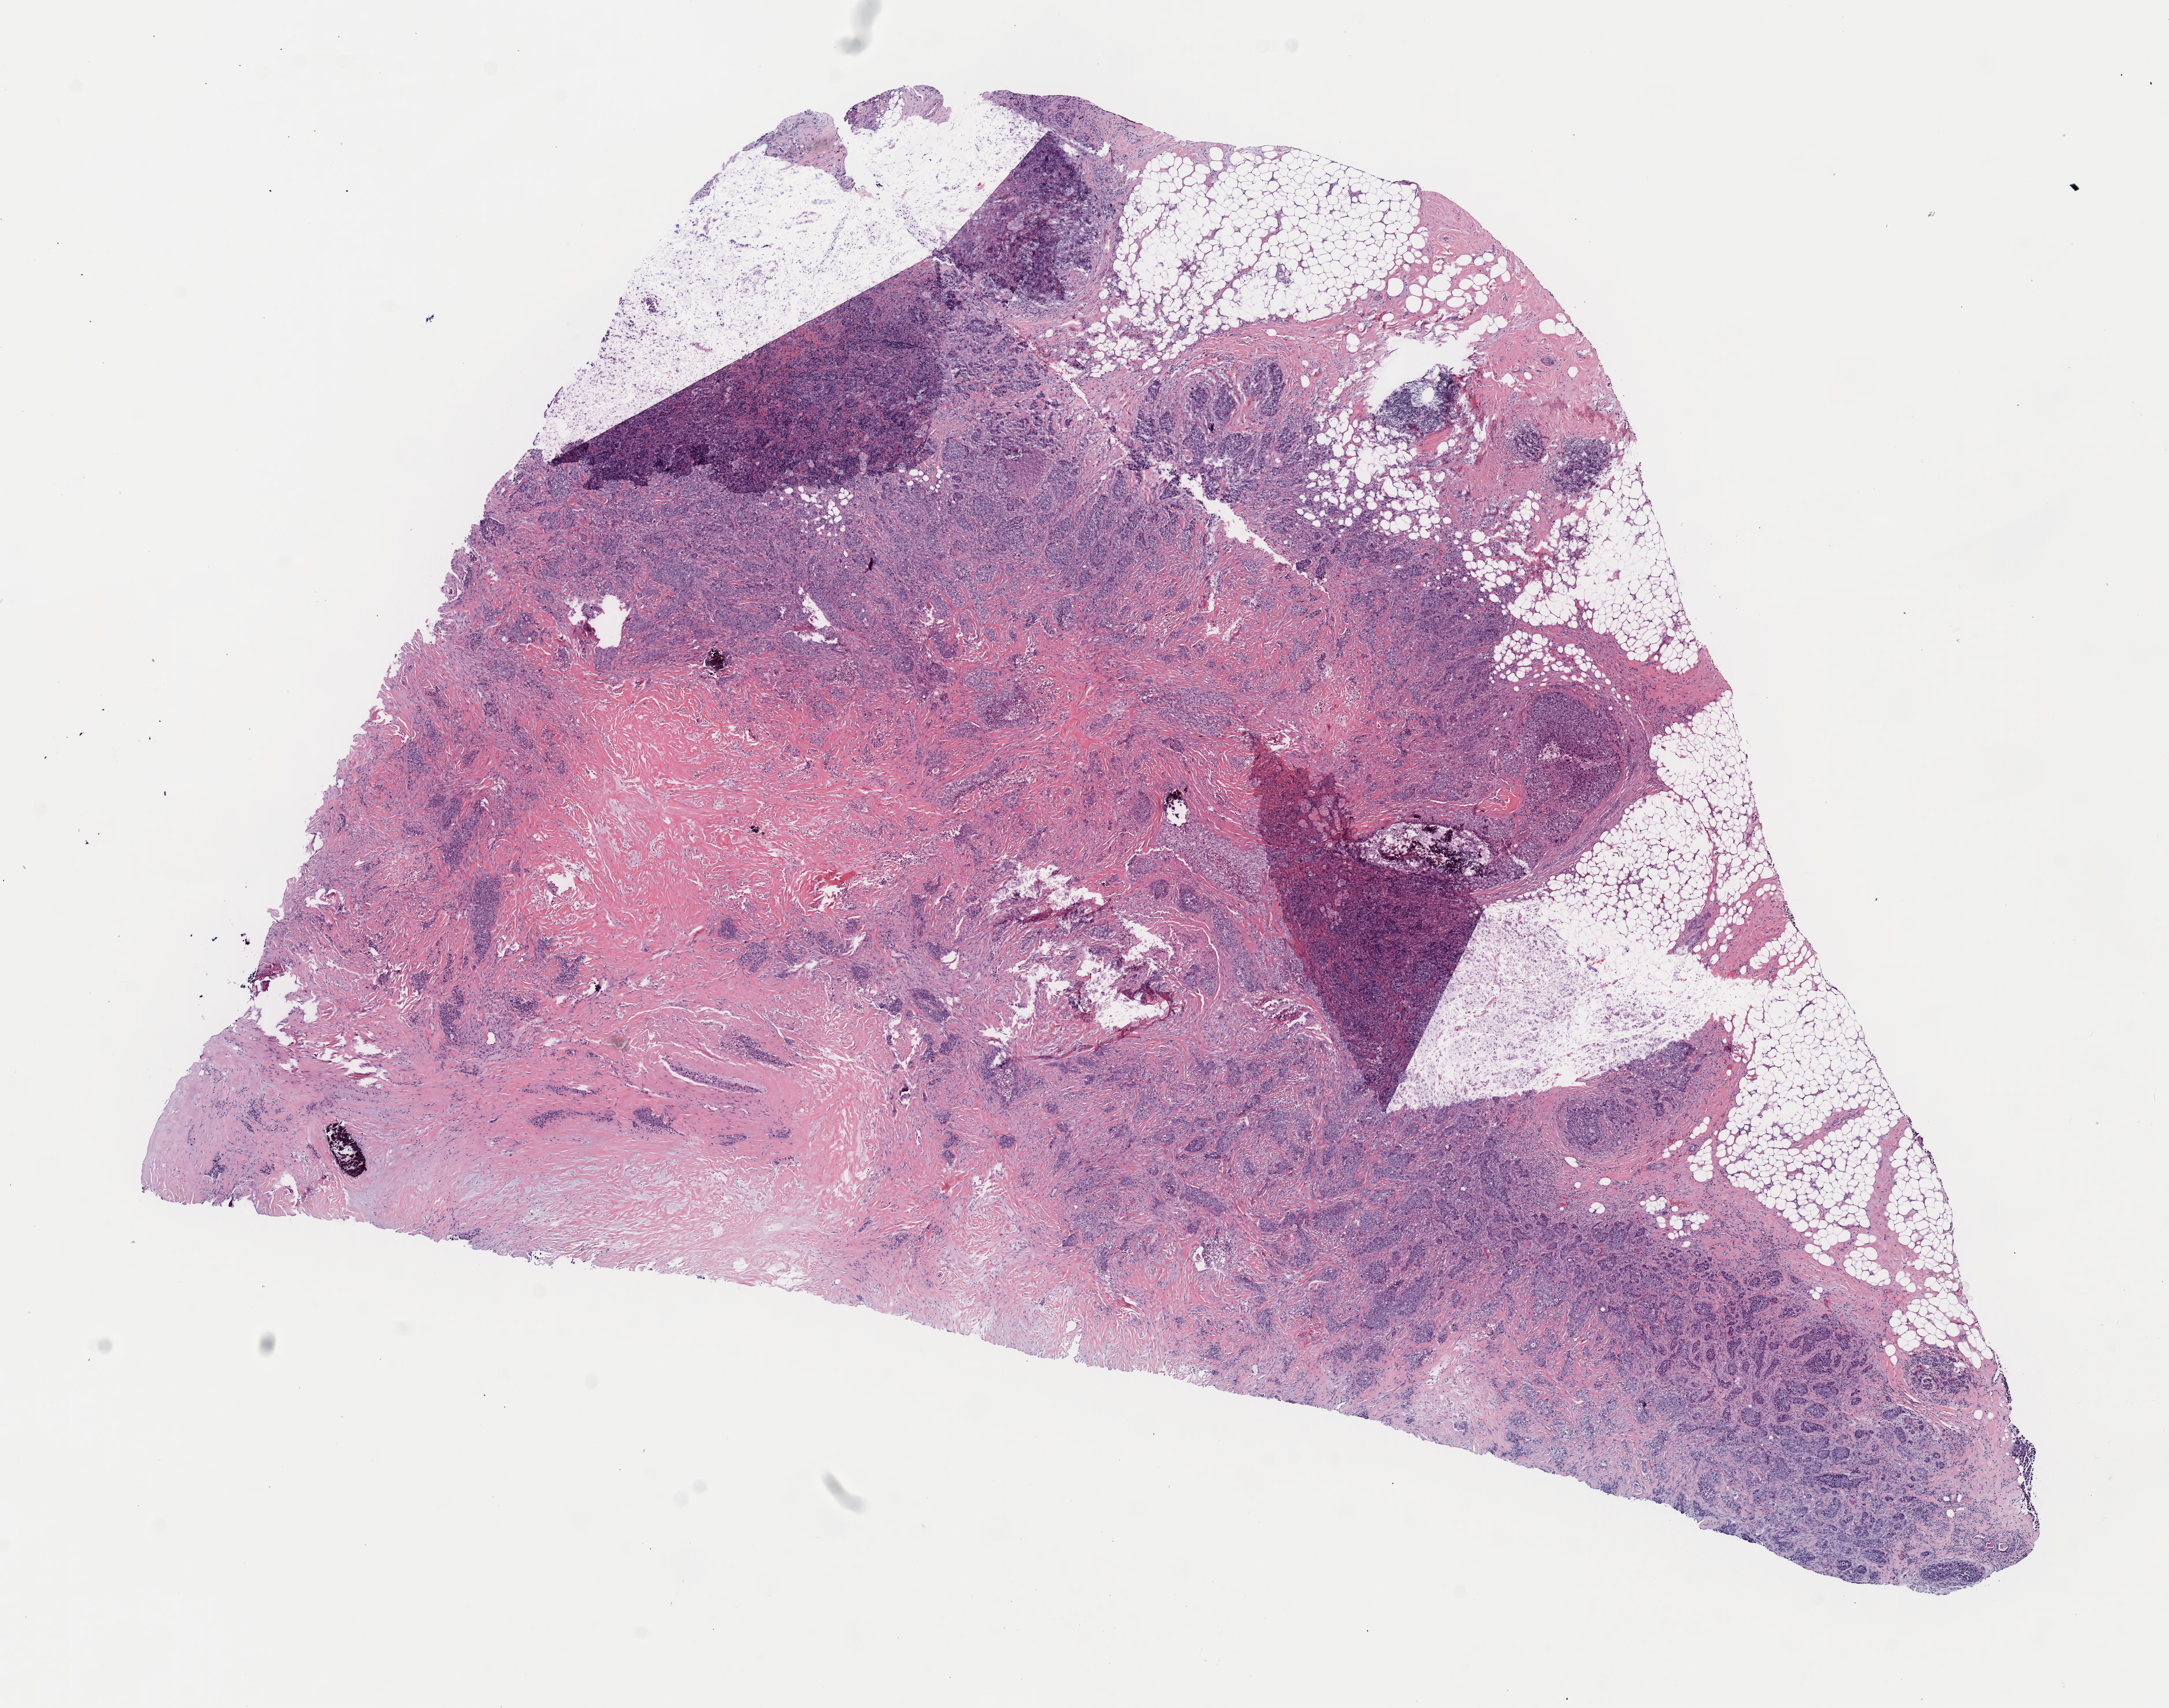
Whole-slide histology image, H&E-stained, a low-resolution overview of the entire scanned area, about 14.8 x 11.7 mm (from a 40x scan); formalin-fixed paraffin-embedded (FFPE) diagnostic section; breast, primary tumour sample. Patient: female, age at initial diagnosis 51 years.
- diagnosis: Infiltrating duct carcinoma, NOS
- laterality: right
- AJCC pathologic stage: IIA (7th edition)
- lymph nodes positive (case pathology): 0 of 5 examined